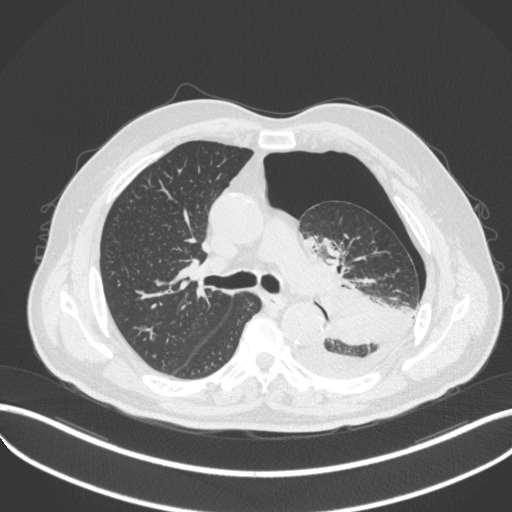
Chest CT, one axial slice; 120 kVp; lung window (W 1500 / L -600 HU); 1 mm slice thickness; 512 × 512 image matrix, field of view 400 × 400 mm. Patient: male, 76 years. Case-level facts recorded for this patient, not image findings: clinical TNM (as recorded): T3 N0 M1b.
Annotated regions visible in this slice (bounding box drawn by a radiologist):
- lung tumour (recorded histology: adenocarcinoma): bounding box [x1, y1, x2, y2] px = [314, 282, 405, 349]